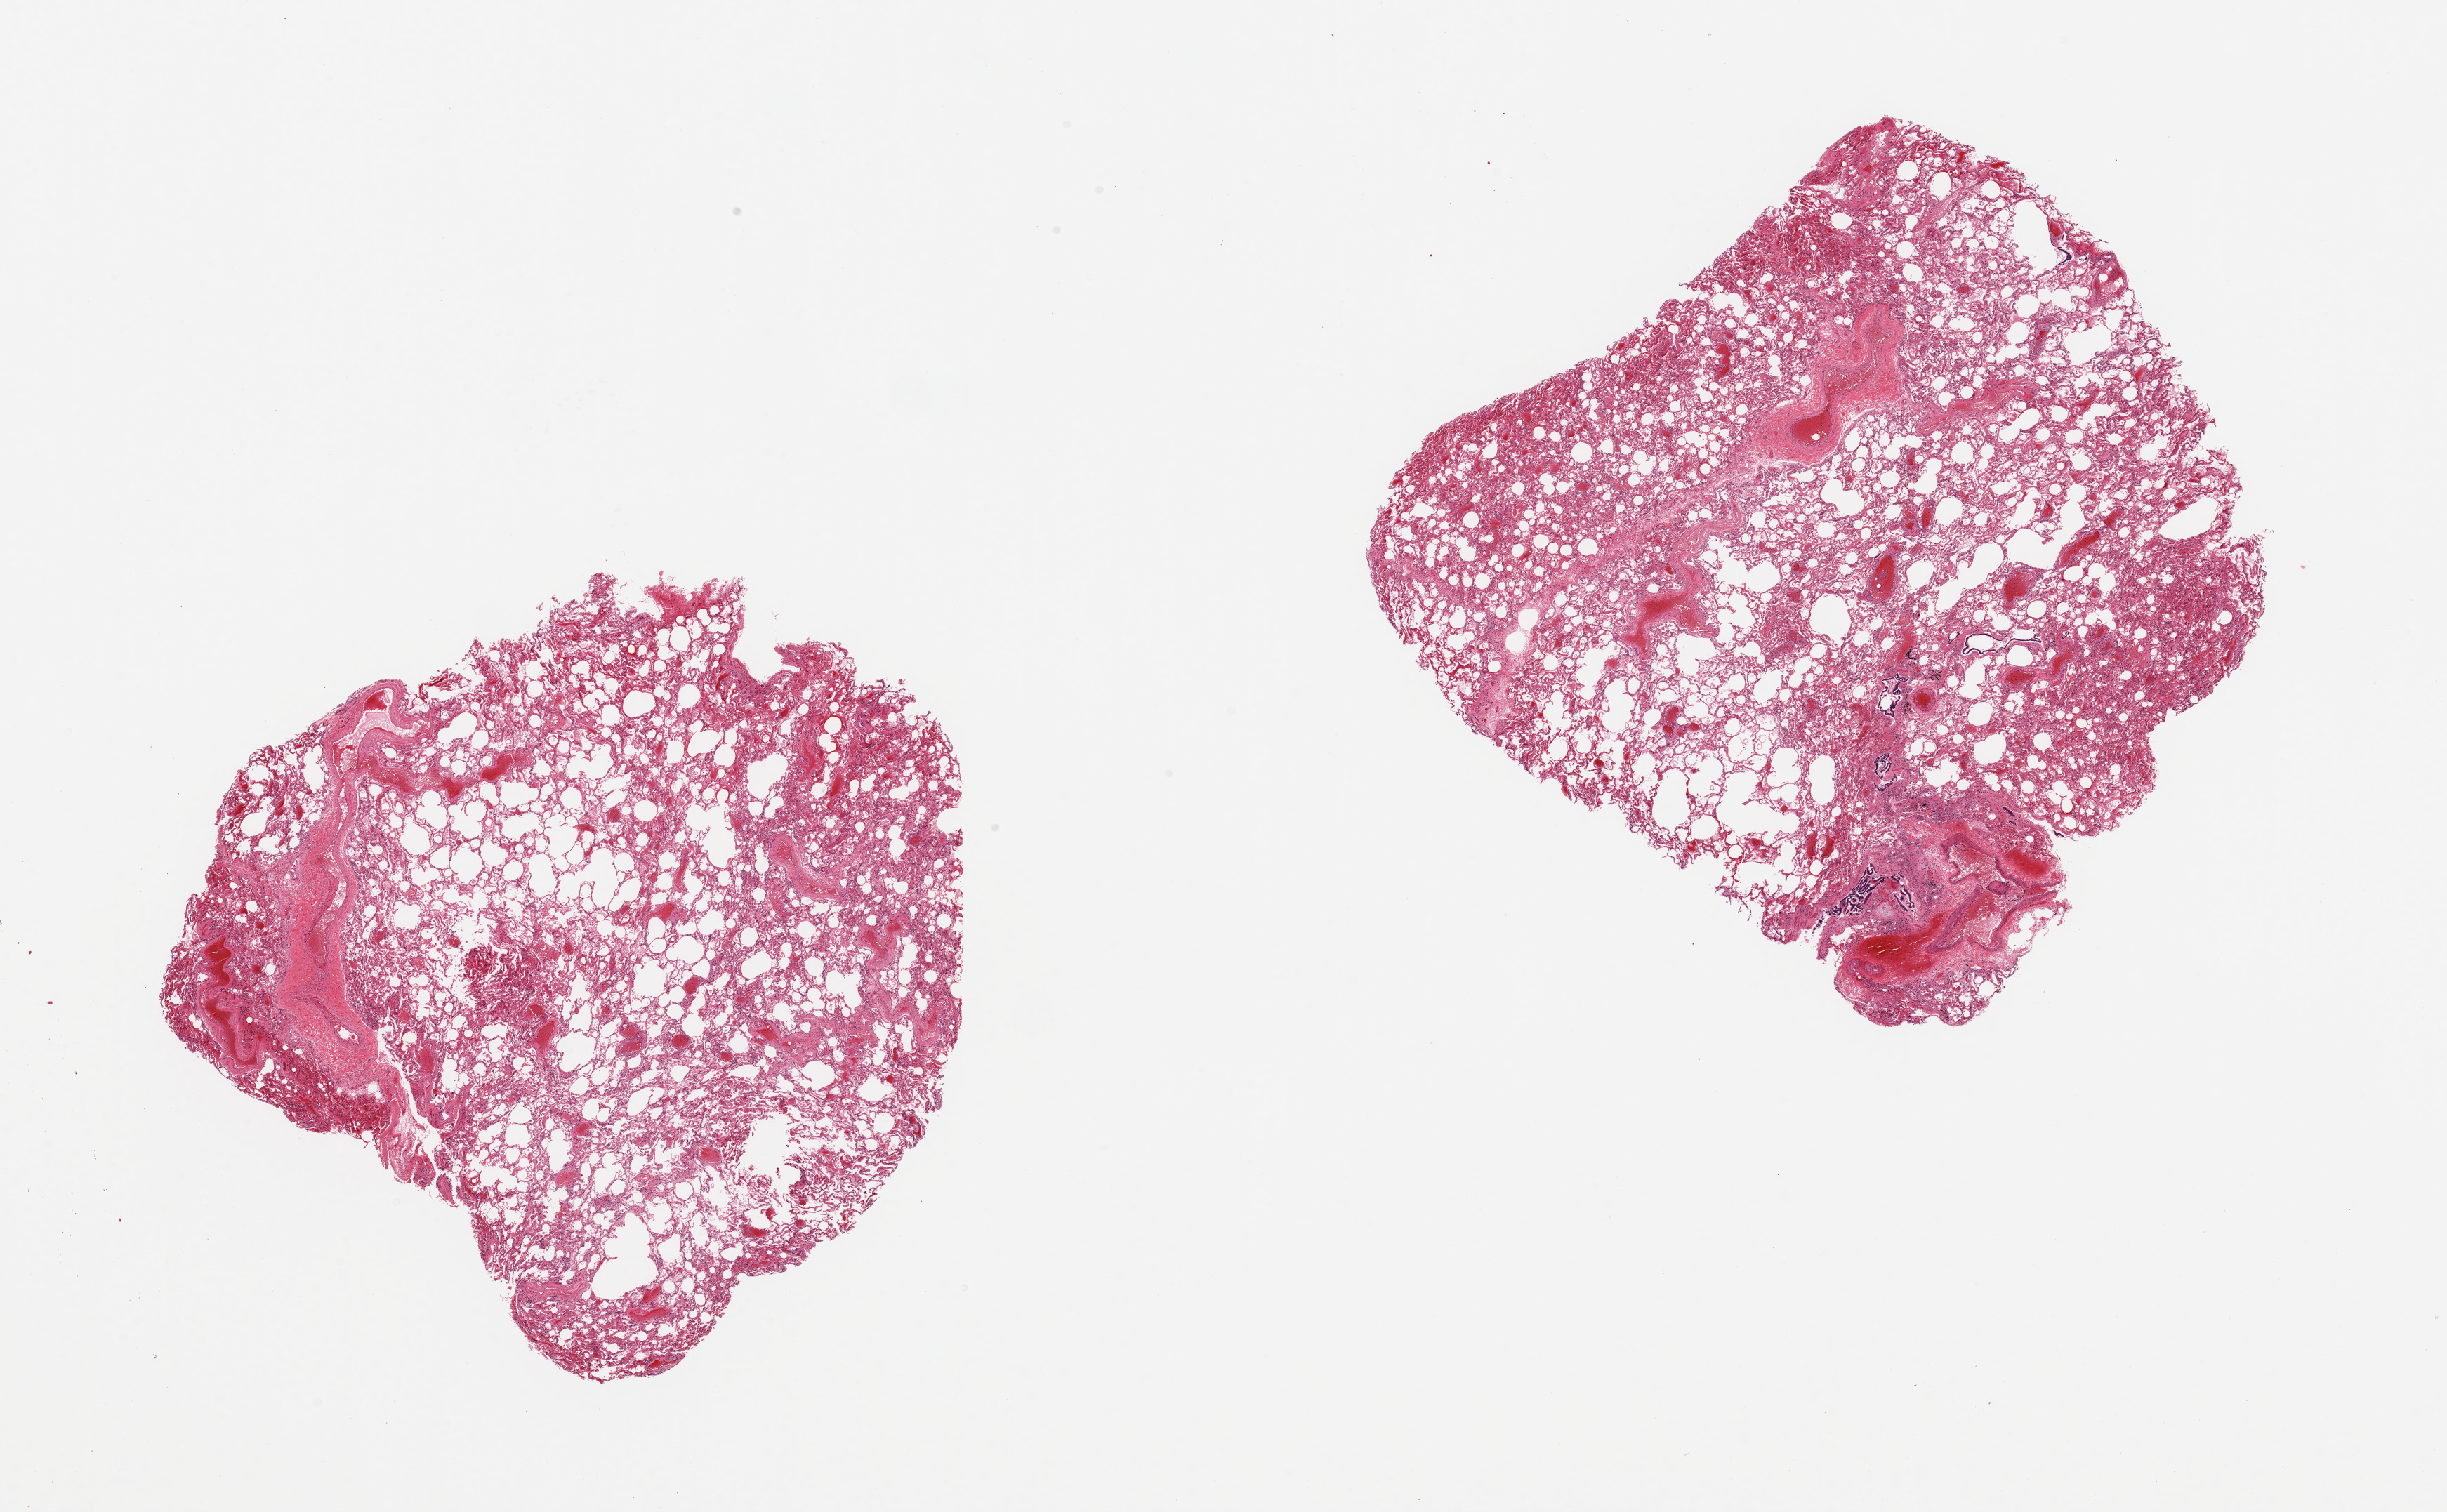
Whole-slide image, hematoxylin and eosin (H&E) stain, brightfield, shown as a low-resolution overview of the whole scanned area (about 27.6 x 17.0 mm); PAXgene-fixed paraffin-embedded (PFPE) section; target tissue: lung; donor tissue sample. Female donor.
Pathologist's review note for this sample: 2 pieces, moderate chronic congestion.